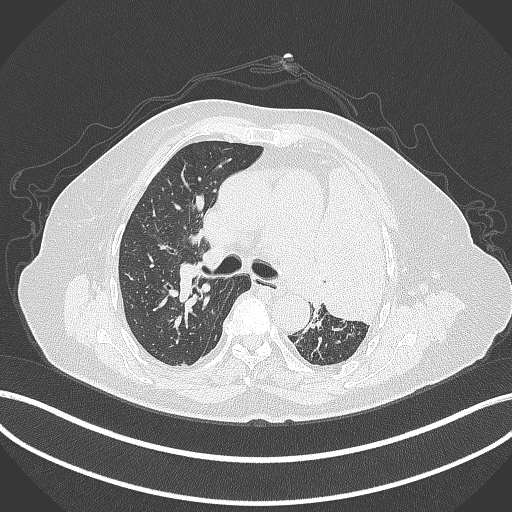
Chest CT, one axial slice. Position 246 of 399 along the scan axis. Reconstruction kernel B70f. 120 kVp. Lung window (W 1500 / L -600 HU). 1 mm slice thickness. 512 × 512 image matrix. Patient: female, 75 years. From the clinical record (not read from this slice): clinical TNM (as recorded): T3 N3 M1.
Structures marked on this image (rectangle marked by the reading radiologist):
- lung tumour (recorded histology: adenocarcinoma): box from (x=310, y=150) to (x=396, y=330) px